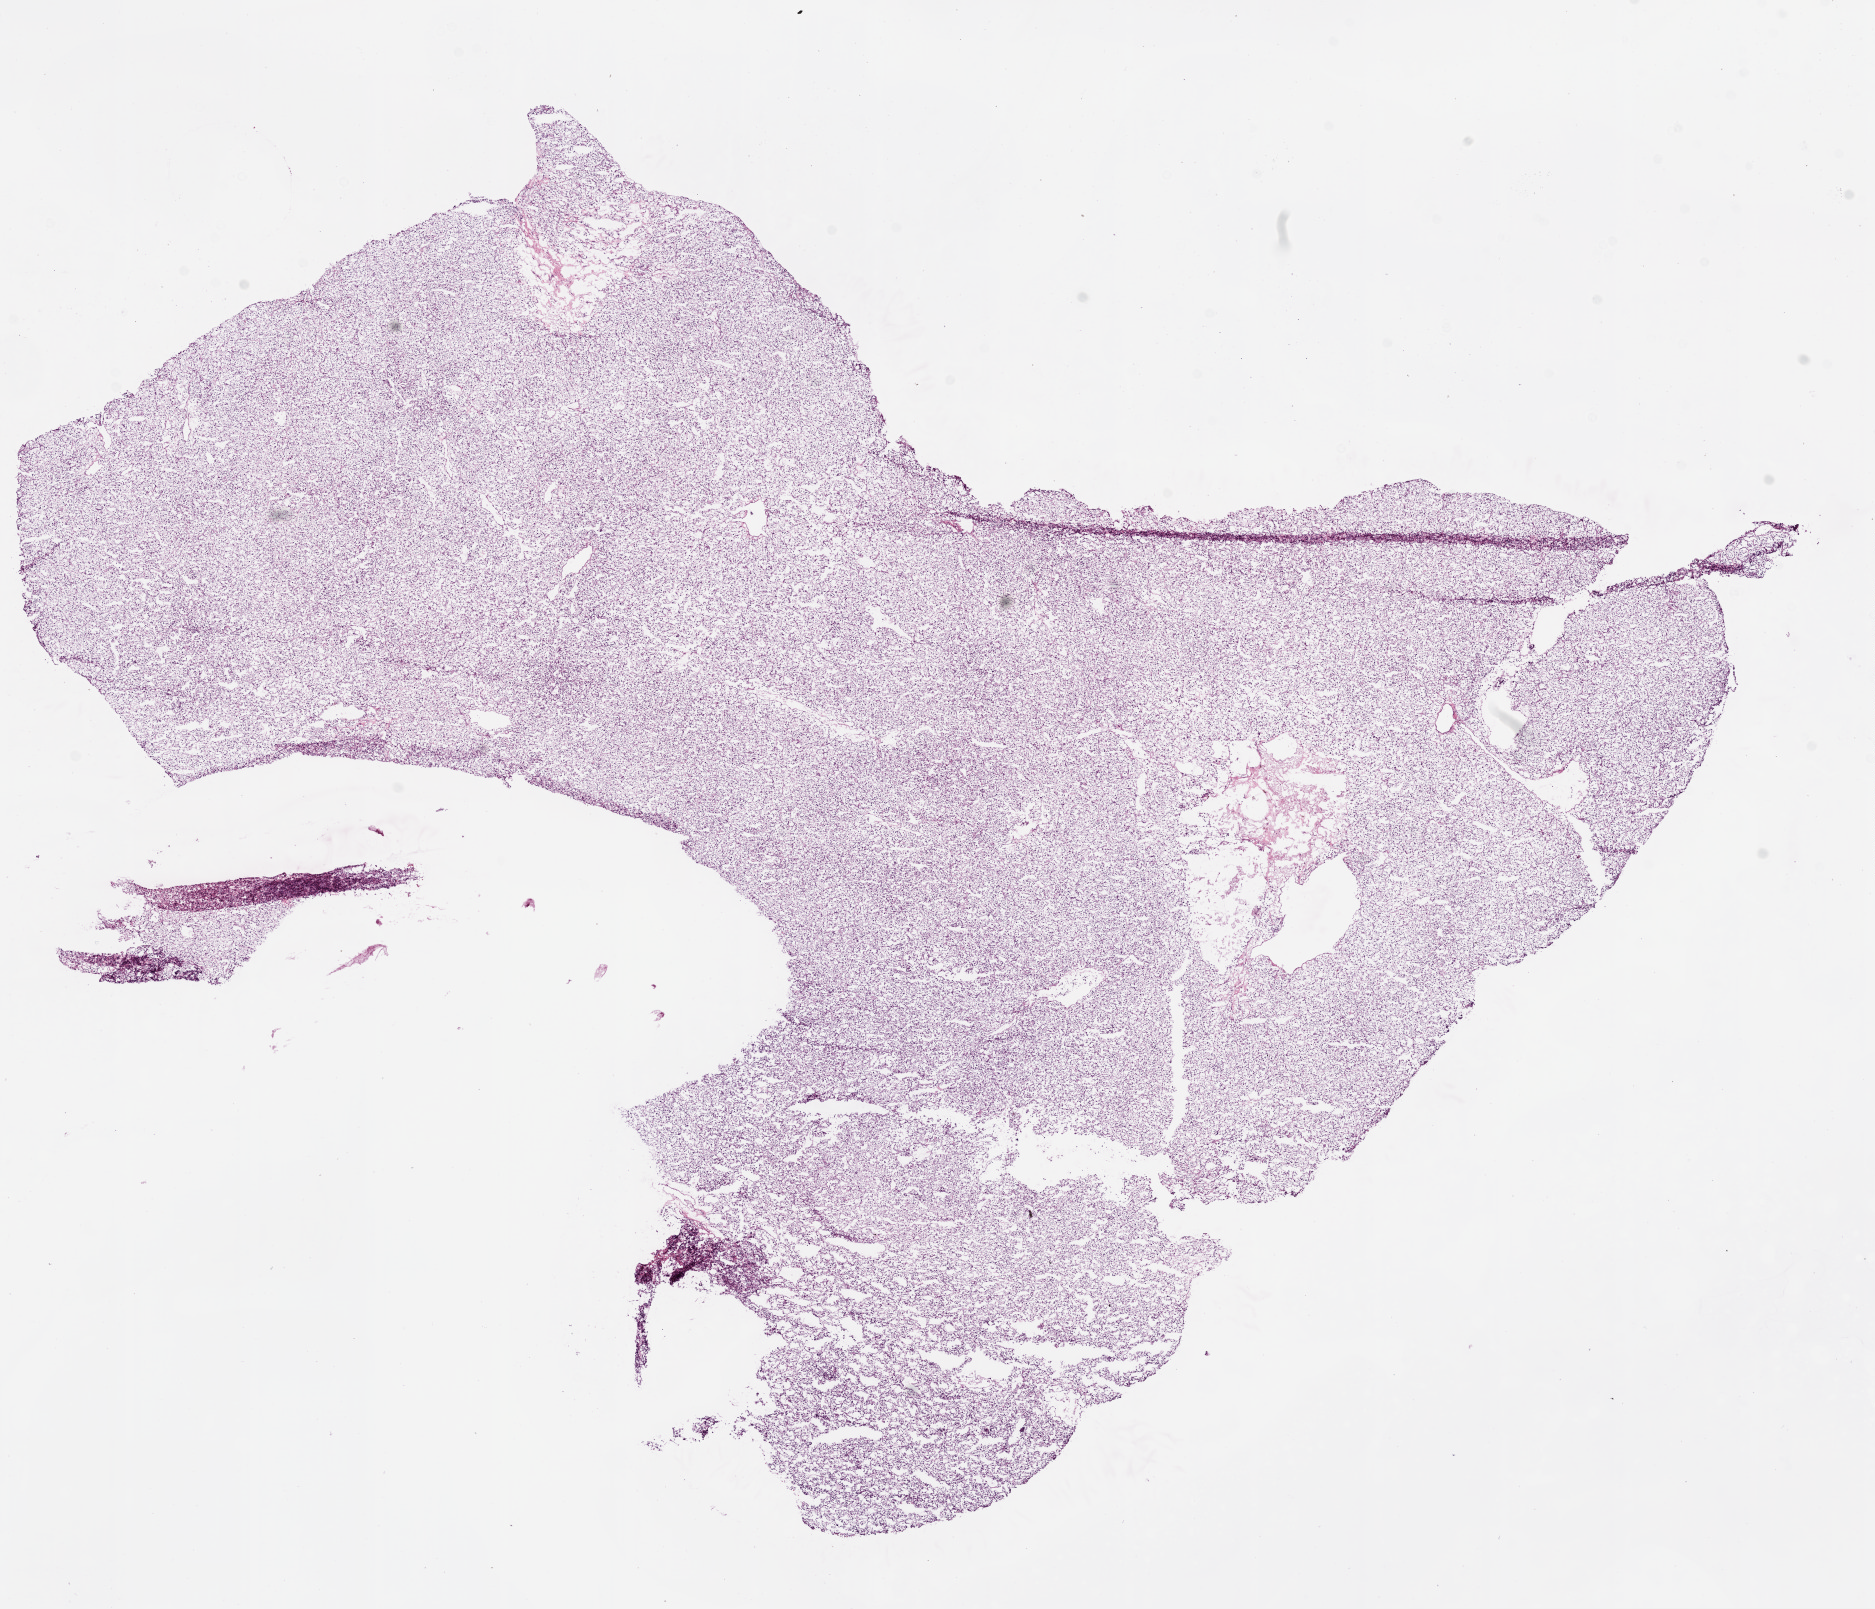
Digitized H&E-stained tissue section (whole slide) — whole scanned area (about 15.0 x 12.9 mm, slide scanned at 20x) shown as a low-resolution overview. Frozen section. Sample: primary tumour, kidney. Patient: female, age at initial diagnosis 59 years. Histologic grade: G2 (moderately differentiated). Pathologist review of this section (percent, as recorded): tumour cells 95%, tumour nuclei 90%, normal cells 0%, stromal cells 5%, necrosis 0%.
AJCC pathologic stage: I. Pathologic diagnosis: Clear cell adenocarcinoma, NOS.